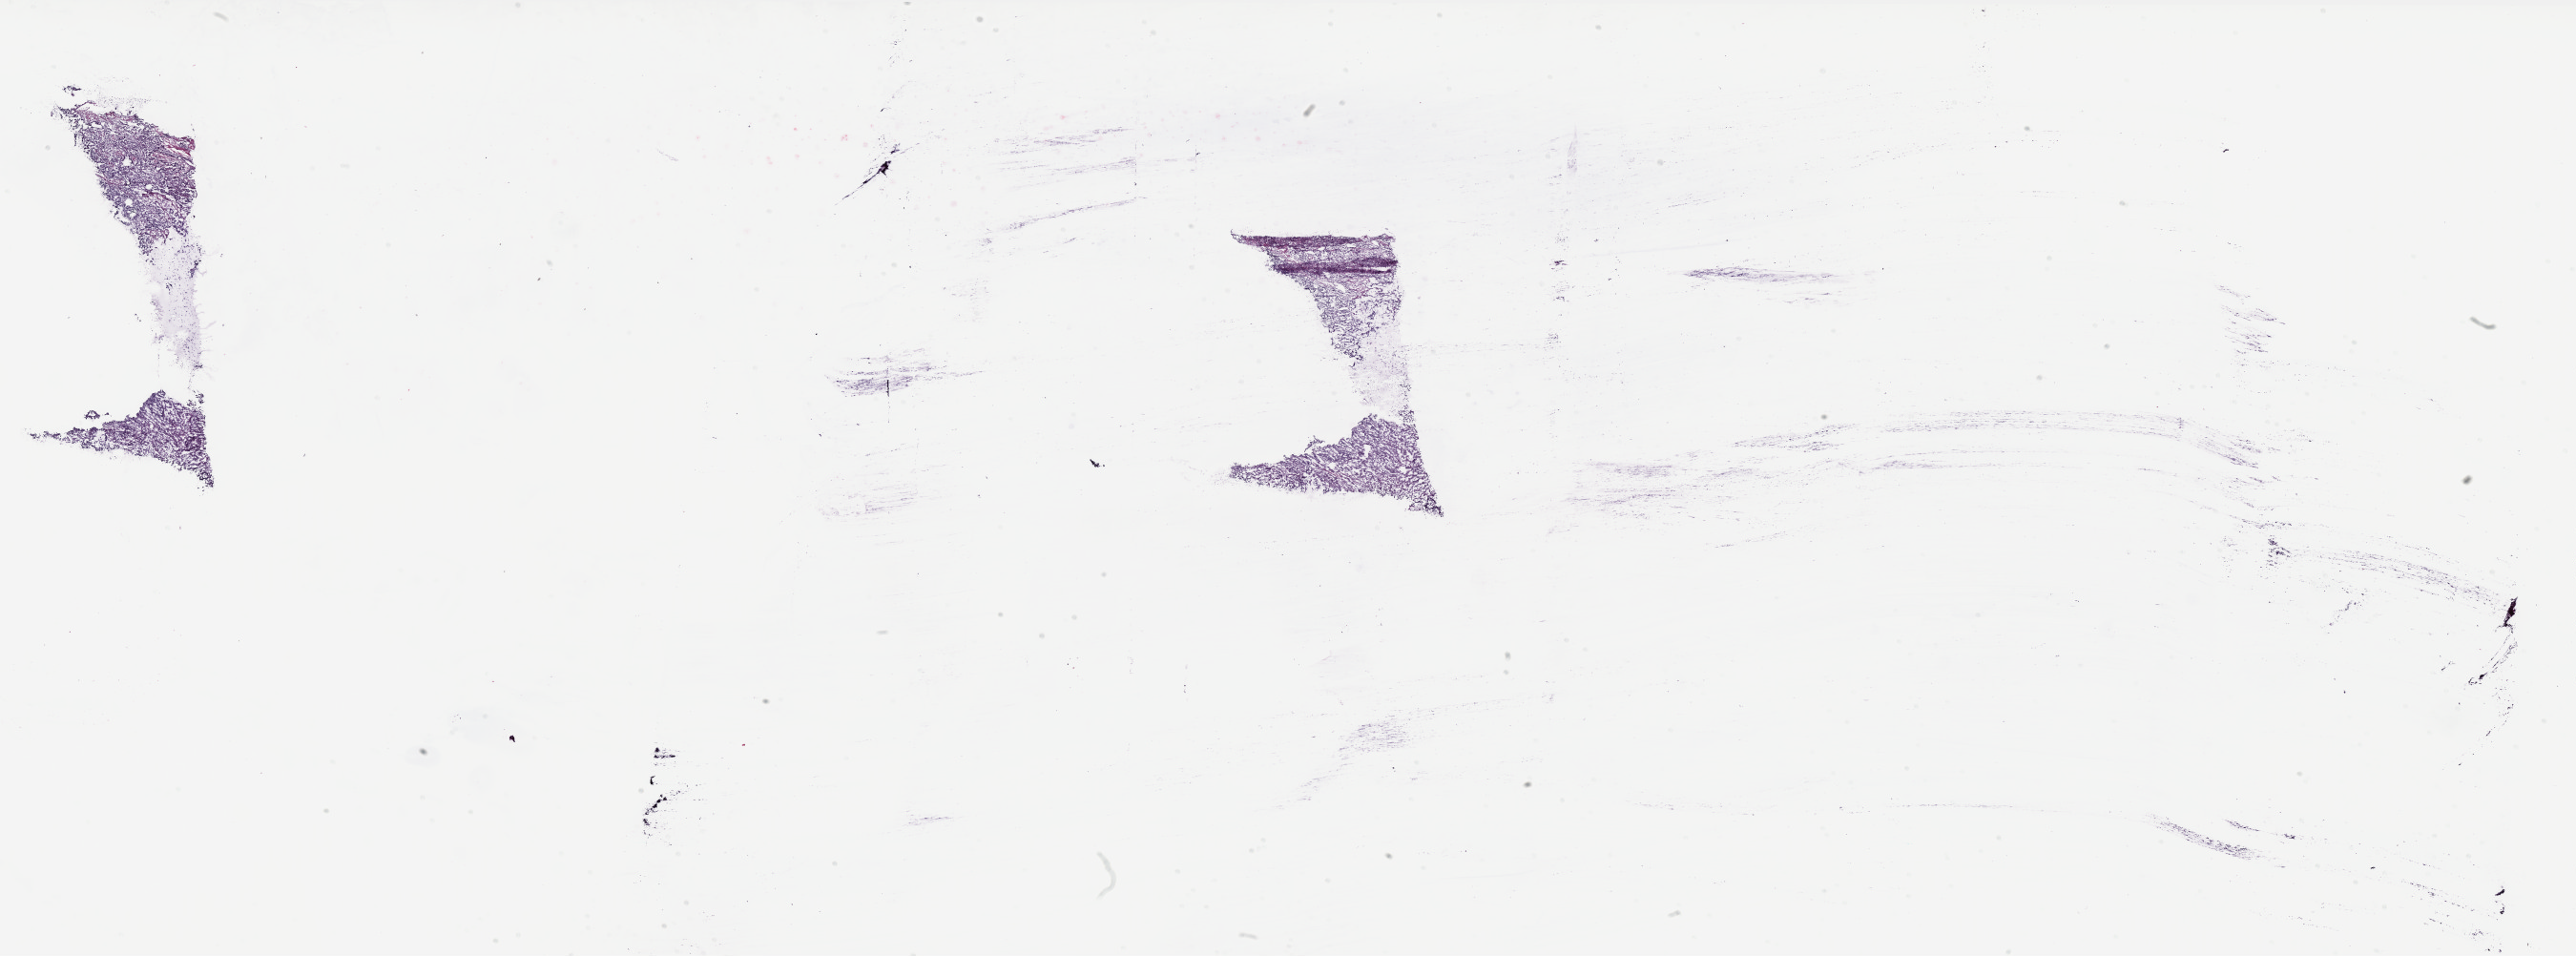
Whole-slide histology image, Hematoxylin and eosin (H&E) stained — whole scanned area (about 43.3 x 16.1 mm, acquisition: 40x scan) shown as a low-resolution overview, frozen section from the bottom of the tissue portion, sample: primary tumour, uterus. Female, age 67 years at initial diagnosis. Histologic grade: G3 (poorly differentiated). Composition of this section per pathologist review: tumour cells 84%, tumour nuclei 80%, normal cells 0%, stromal cells 15%, necrosis 1%. Infiltration values recorded for this section: lymphocyte infiltration 8%, monocyte infiltration 0%, neutrophil infiltration 0%.
• diagnosis: Serous cystadenocarcinoma, NOS (endometrium)
• FIGO stage: IIIC2
• lymph nodes positive (case pathology): 1 of 29 examined